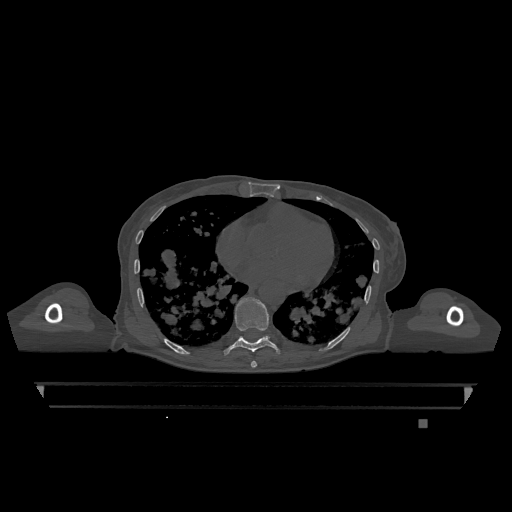
CT including the spine, one axial slice; position 688 of 1317 along the scan axis; bone window (W 1800 / L 400 HU); 0.5 mm slice thickness; 512 × 512 image matrix, field of view 500 × 500 mm. Female patient, age 74 years. From the clinical record (not read from this slice): primary cancer: lung.
Outlined on this slice (semi-automatically segmented with operator editing):
- T7 vertebra: bounding box [x1, y1, x2, y2] px = [251, 361, 257, 368]
- T9 vertebra: [223, 297, 281, 356]